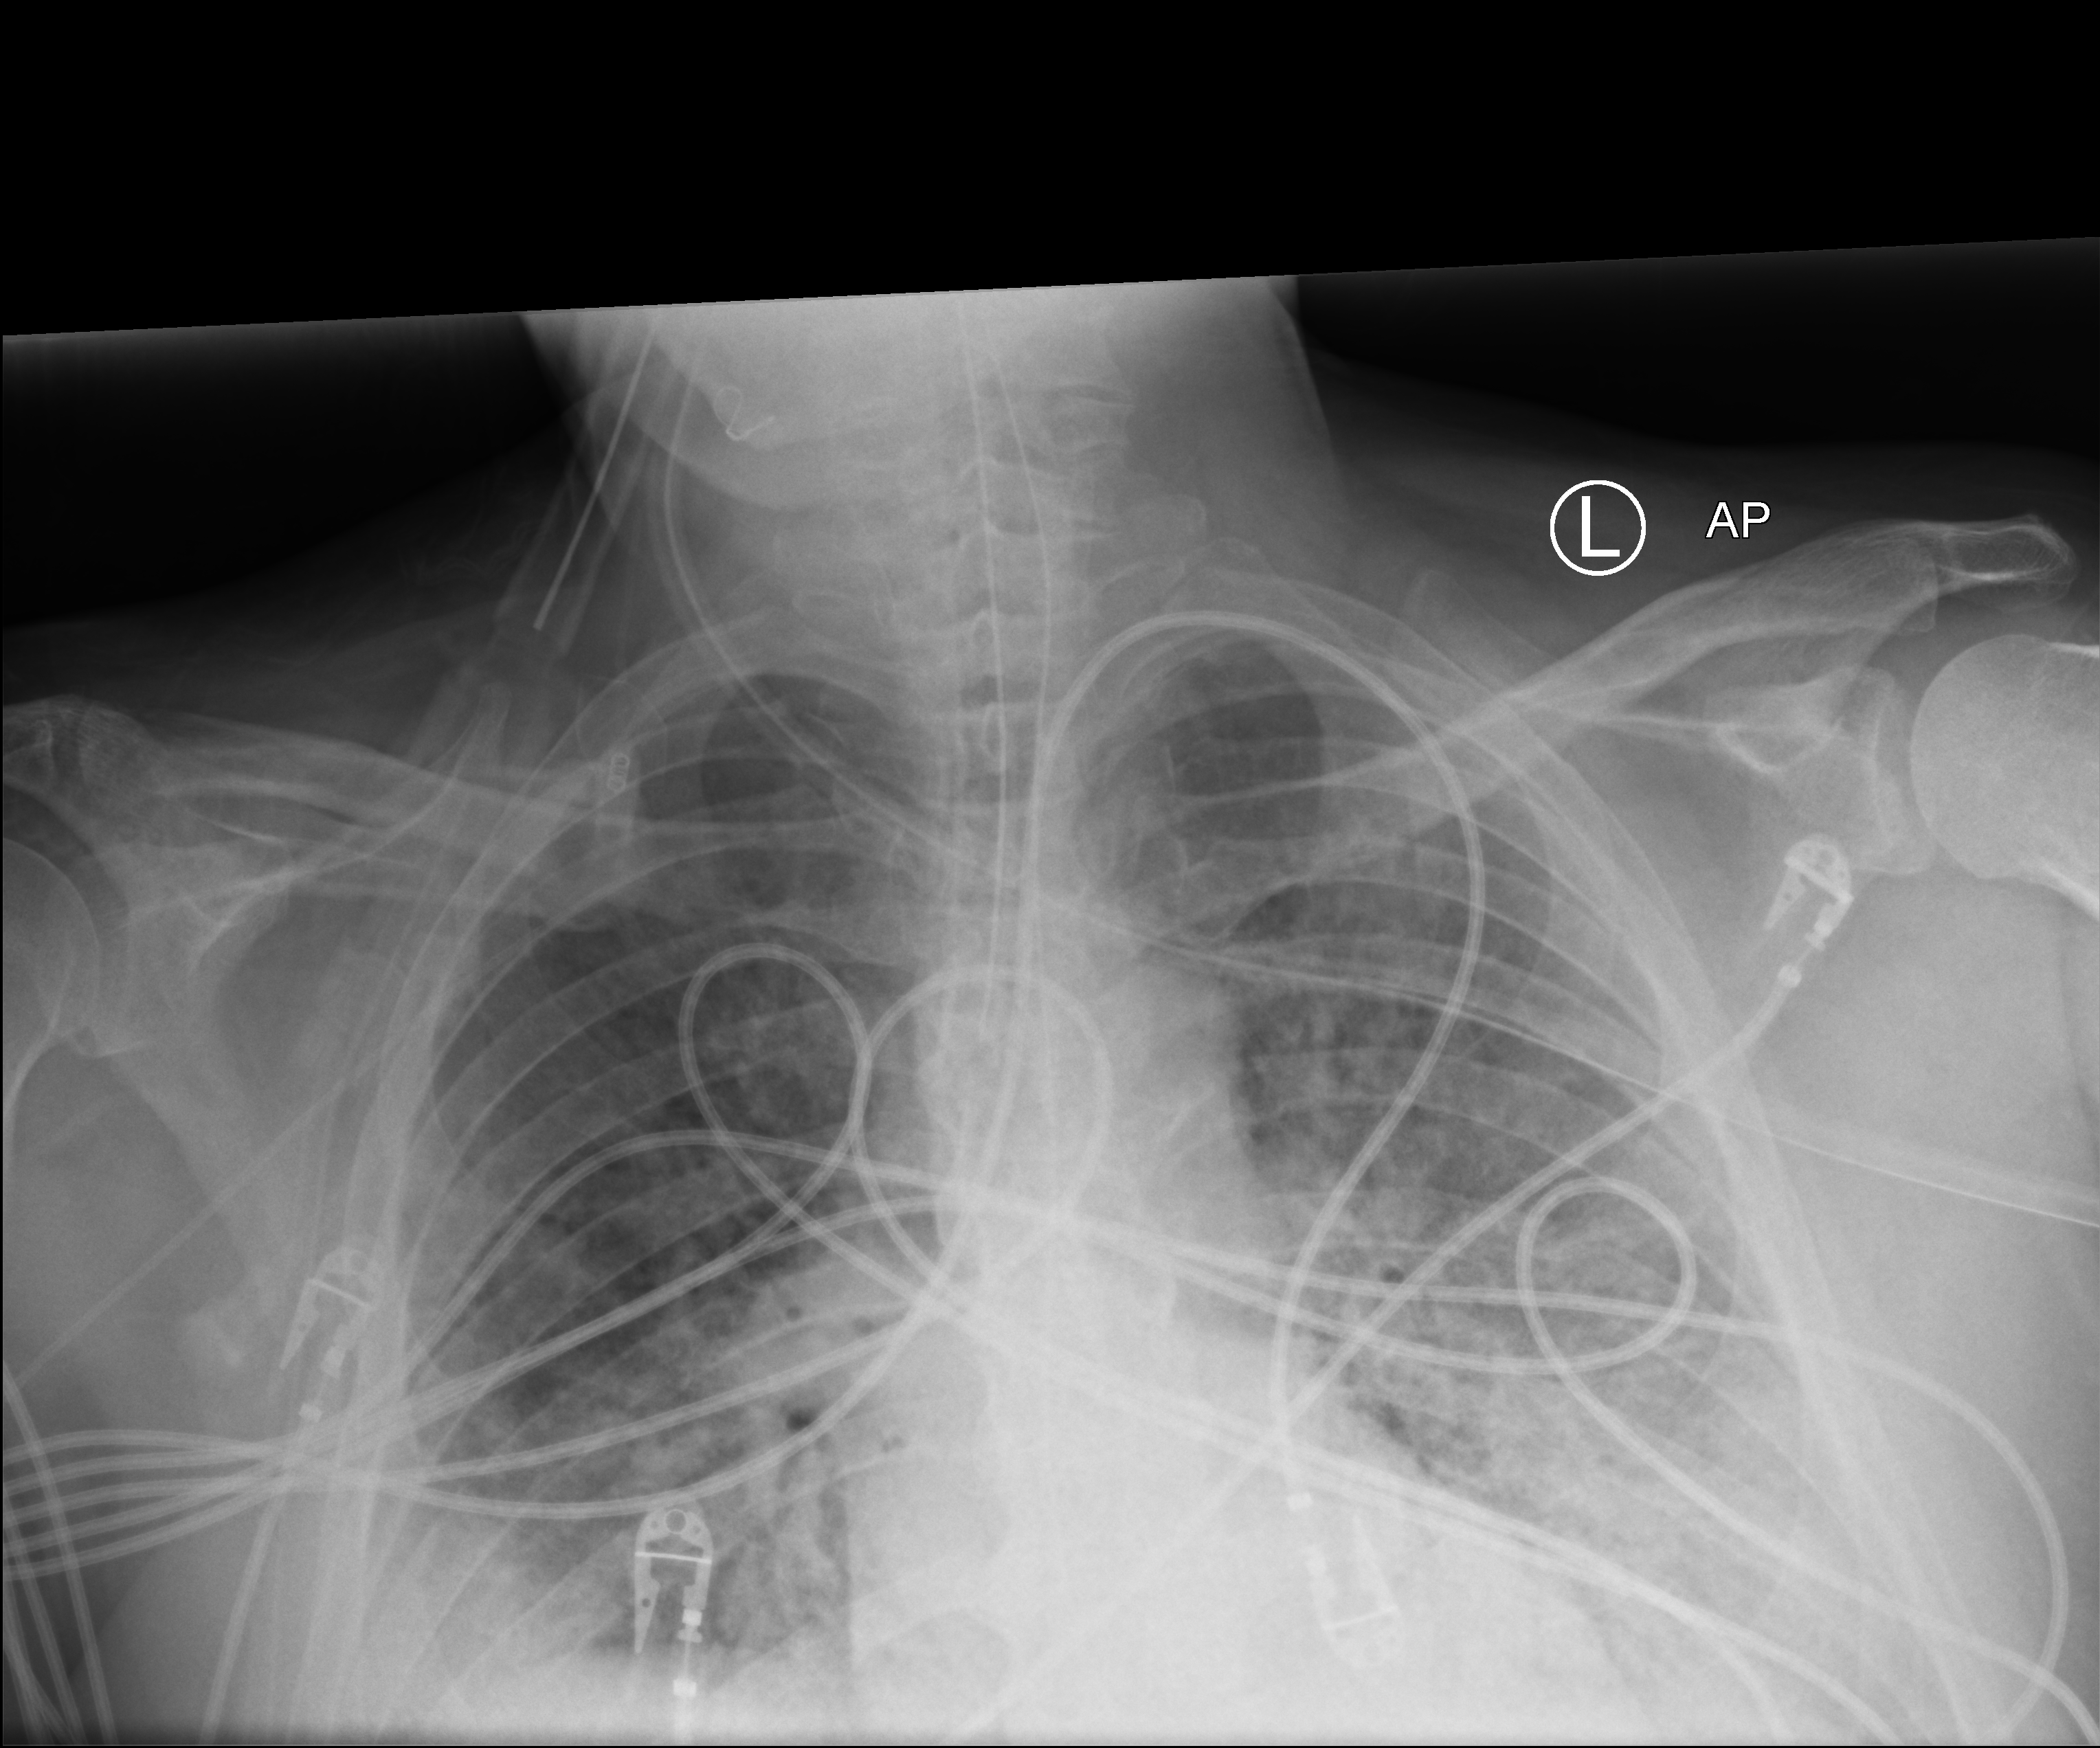
Bedside chest radiograph (computed radiography), anteroposterior (AP) projection. Patient hospitalised with COVID-19; male, aged 60–74 years.
Admission-level facts for this patient (not findings on this image; timing relative to this image not recorded):
- admitted to intensive care during this hospital stay: yes
- hypertension (admission record): yes